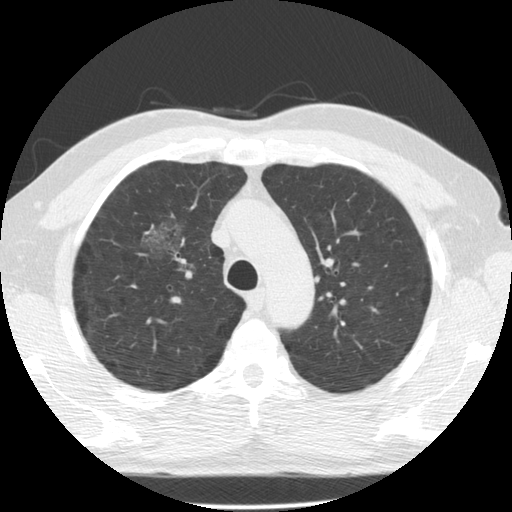
Chest CT (low-dose screening protocol), one axial image. Second annual screen. Lung window (W 1500 / L -600 HU). 2.5 mm slice thickness. 140 kVp. Slice 96 of 135 in the series. 512 × 512 image matrix. Male, age 60 years at enrolment. Former smoker at enrolment.
Lesion marked by an expert reader, bounding box (x1, y1, x2, y2) in pixels: (133, 212, 199, 274). Screening reader's record for this exam (one nodule recorded; not confirmed to be the boxed lesion): non-calcified nodule or mass ≥4 mm, right upper lobe, poorly defined margins, mixed attenuation, pre-existing on the prior screen: yes; interval growth: yes. Official screen result: positive, other.